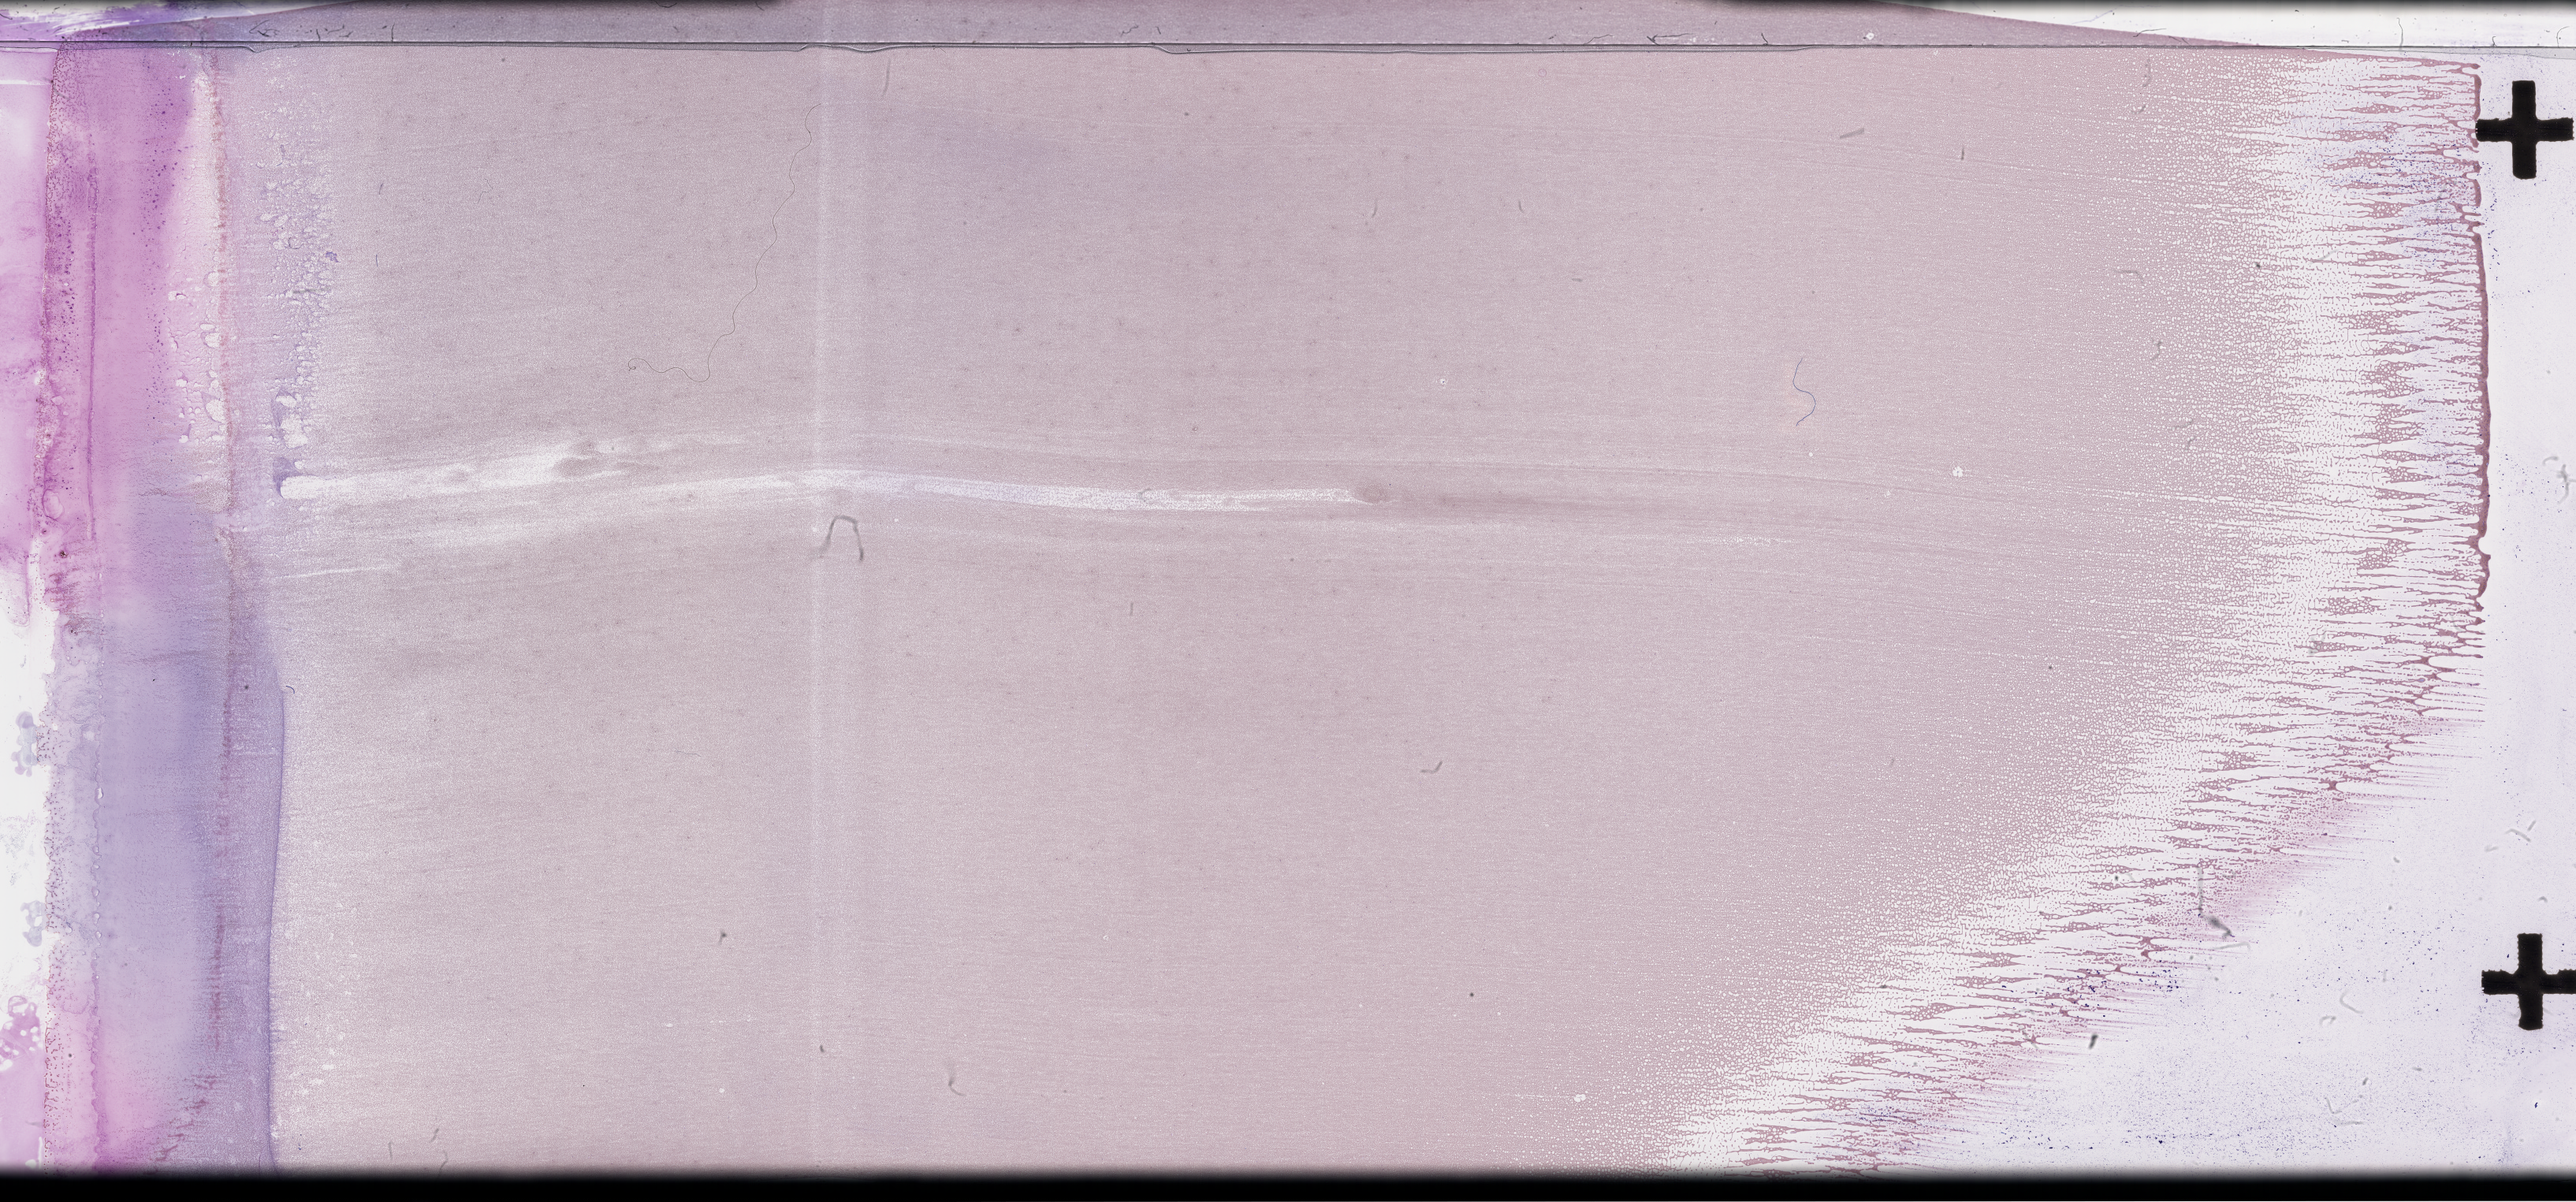
Whole-slide image of a whole blood smear, Wright-Giemsa stain, shown as a low-resolution overview of the whole scanned area (about 52.8 x 24.6 mm). Smear from an EDTA sample. Specimen time point: collected on treatment. Patient sex: male.
• from a patient with: Plasma Cell Myeloma